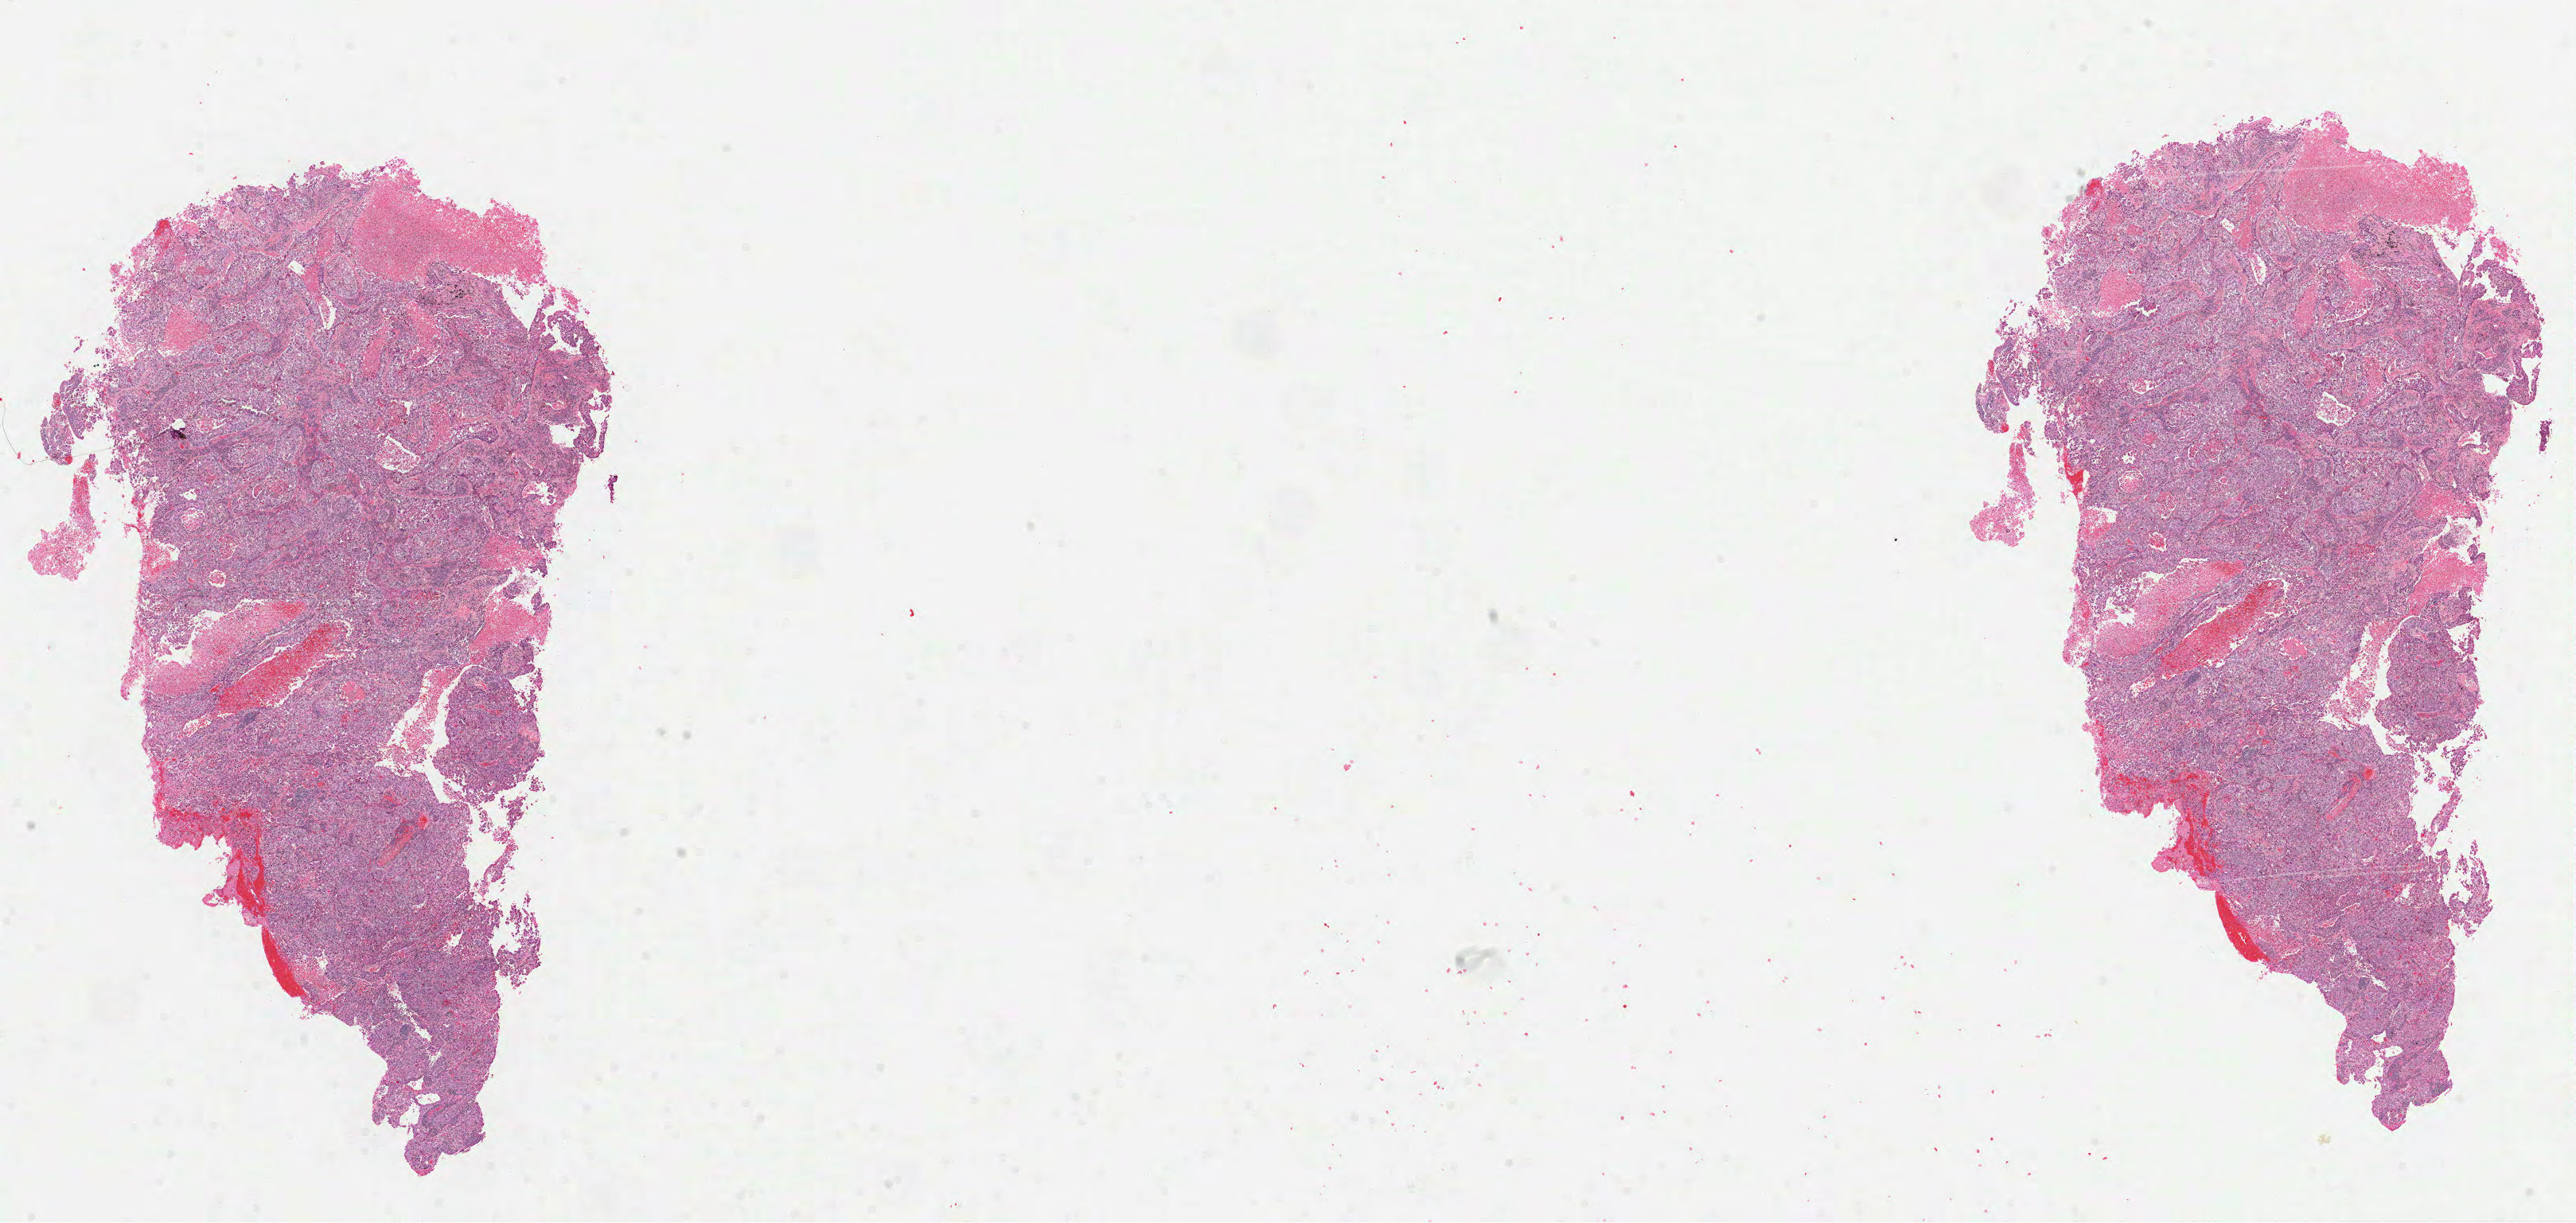
H&E-stained whole-slide image, shown as a low-resolution overview of the whole scanned area (about 26.1 x 12.4 mm, acquisition: 40x scan); formalin-fixed paraffin-embedded (FFPE) diagnostic section; sample: primary tumour, lung. Female, age 72 years at initial diagnosis.
- laterality: left
- AJCC pathologic stage: IB
- pathologic diagnosis: Adenocarcinoma, NOS (upper lobe, lung)